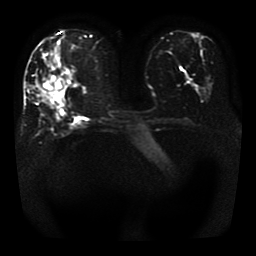
Breast MRI, one axial slice; slice 16 of 41 in the series (ordered by position); diffusion-weighted series; image 2 of 4 stored at this slice position (different b-values; order by instance number); 1.5 T; 5 mm slice thickness; 256 × 256 image matrix, field of view 330 × 330 mm. Female patient.
Structures marked on this image (outlined manually by an expert reader):
- tumour on diffusion-weighted imaging: bounding box [x1, y1, x2, y2] px = [45, 83, 60, 90]